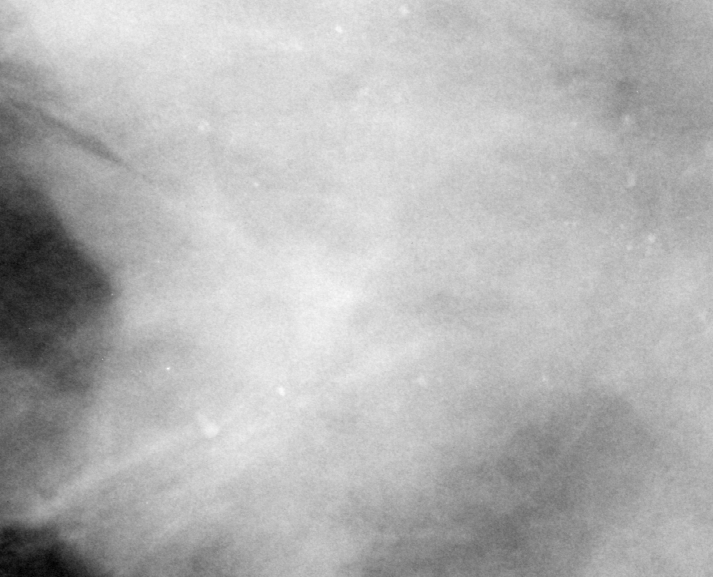
Region of interest cut from a scanned film mammogram (one marked finding); left breast; CC view; BI-RADS breast density category 4 (scale 1–4).
Finding: calcifications, morphology round and regular / punctate / amorphous, distribution regional; BI-RADS assessment category 3; pathology result (as recorded, not read from the image): benign.